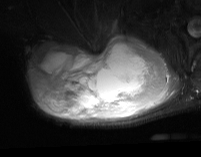
MRI of an extremity soft-tissue mass, one axial slice. STIR. MR volume resampled by the dataset authors to the PET/CT grid (not the native acquisition matrix). 201 × 157 image matrix. Male patient. Case-level facts recorded for this patient, not image findings: histological type: pleiomorphic spindle cell undifferentiated; grade: high; site of the primary tumour: right parascapusular.
Annotated regions visible in this slice (expert contour drawn on MRI and transferred to this co-registered scan by the dataset authors):
- gross tumour volume including surrounding oedema: bounding box <28,36,182,122> (left, top, right, bottom; pixels)
- gross tumour volume (mass): <30,36,169,119>